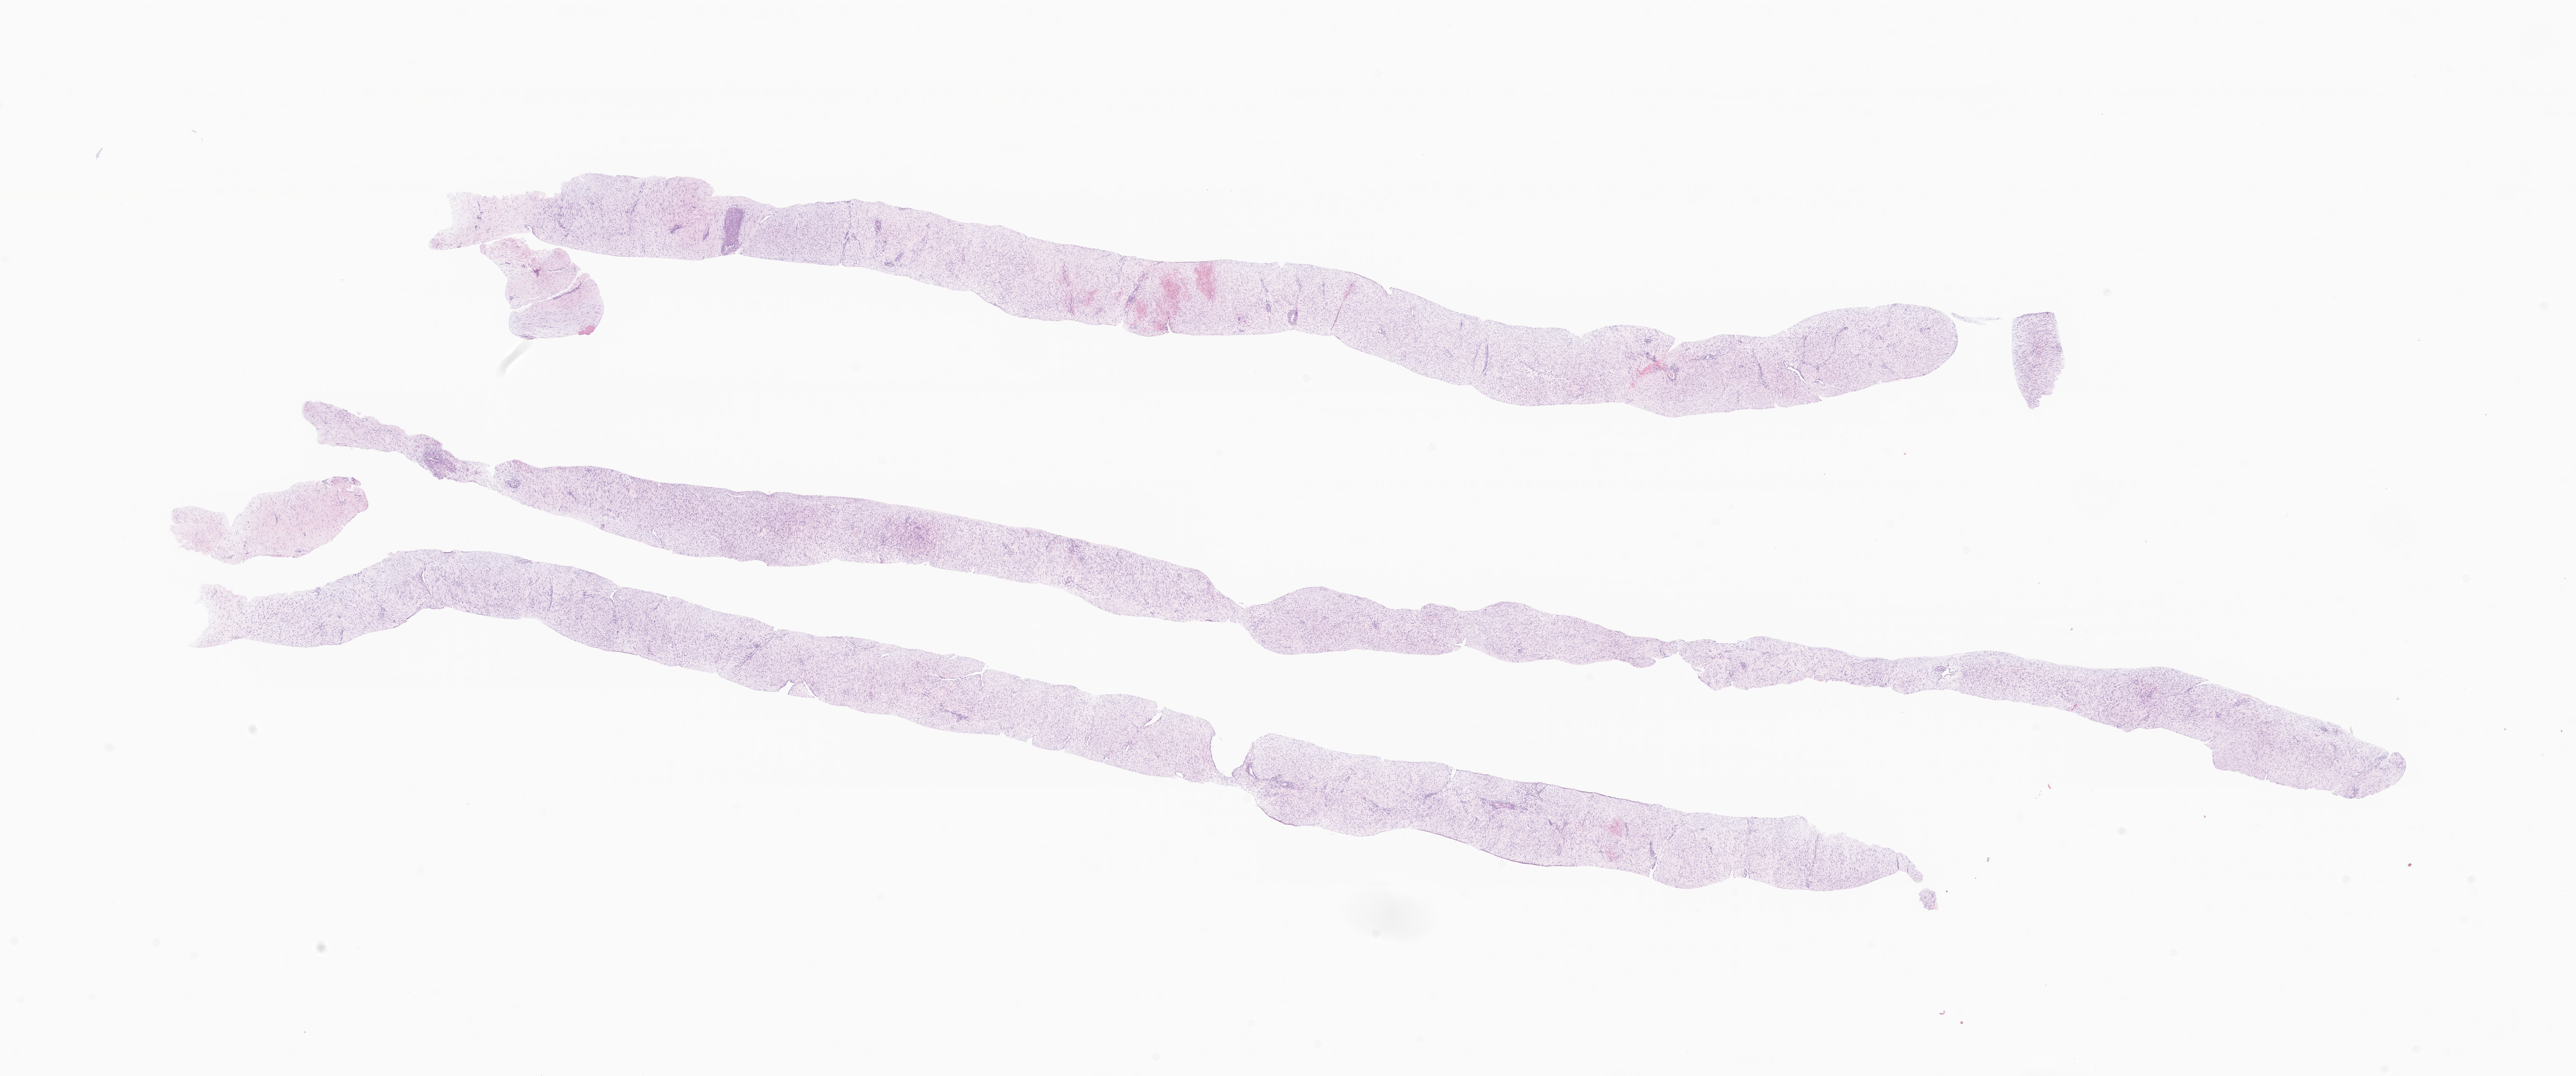
Whole-slide image, hematoxylin and eosin (H&E) stain of tumor tissue from the soft tissue of thorax, whole scanned area (about 27.9 x 11.7 mm) shown as a low-resolution overview. Formalin-fixed paraffin-embedded section. Patient male; age 204 months.
• diagnosis: Aggressive fibromatosis
• tissue or organ of origin (case record): connective, subcutaneous and other soft tissues of thorax